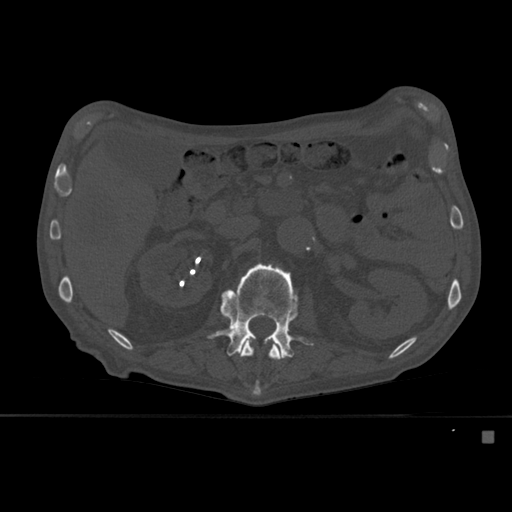
CT including the spine, one axial slice. Slice 241 of 527 in the series (ordered by position). Bone window (W 1800 / L 400 HU). 1.5 mm slice thickness. 512 × 512 image matrix. Patient: male, 78 years. From the clinical record (not read from this slice): primary cancer: prostate.
Annotated regions visible in this slice (semi-automatic segmentation, software-assisted and operator-edited):
- L1 vertebra: box from (x=241, y=339) to (x=283, y=396) px
- L2 vertebra: (x=208, y=263)–(x=314, y=358)